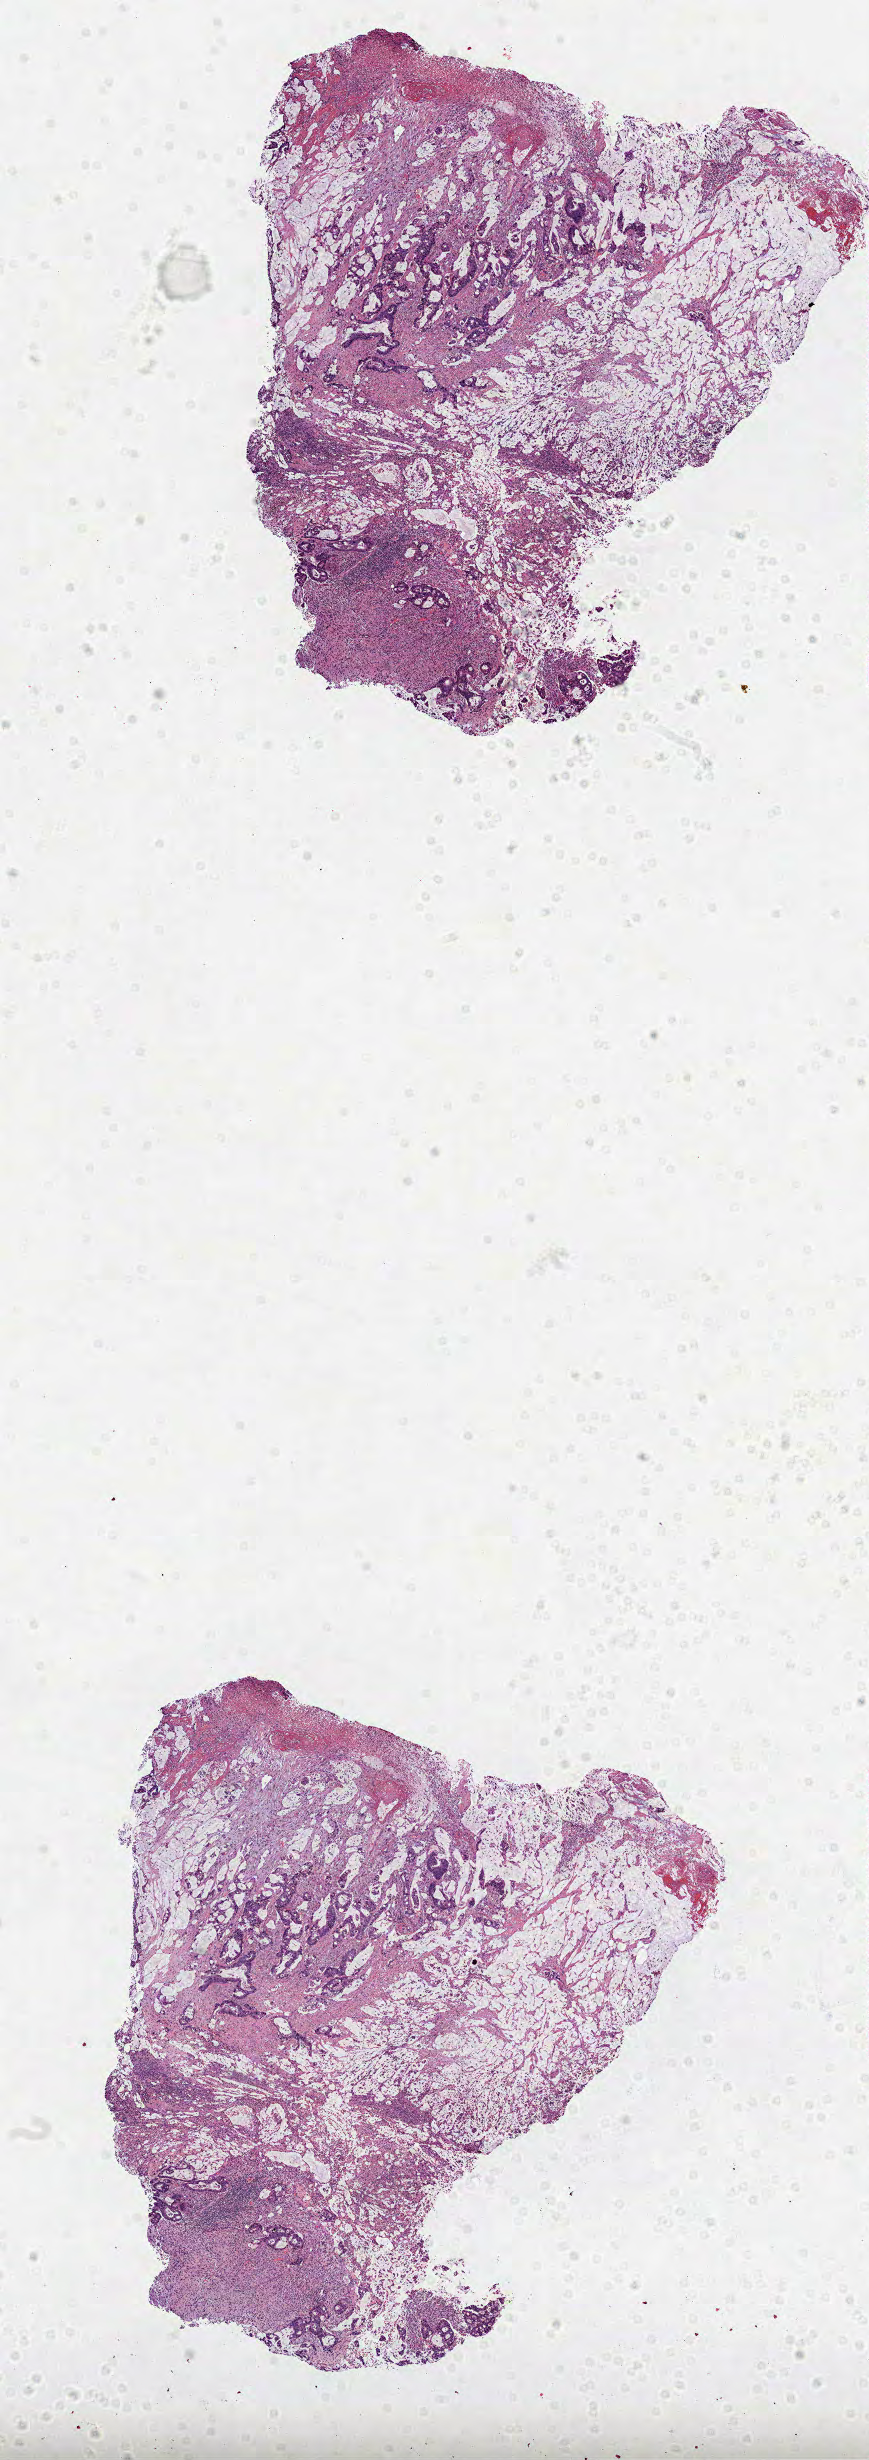
Whole-slide histology image, H&E-stained, low-resolution overview of the scanned area, about 7.0 x 19.8 mm; FFPE section; primary tumour sample from the colon. Patient: male, age at initial diagnosis 71 years.
• lymph nodes positive (case pathology): 7 of 20 examined
• AJCC pathologic stage: IV
• histologic diagnosis: Mucinous adenocarcinoma (sigmoid colon)